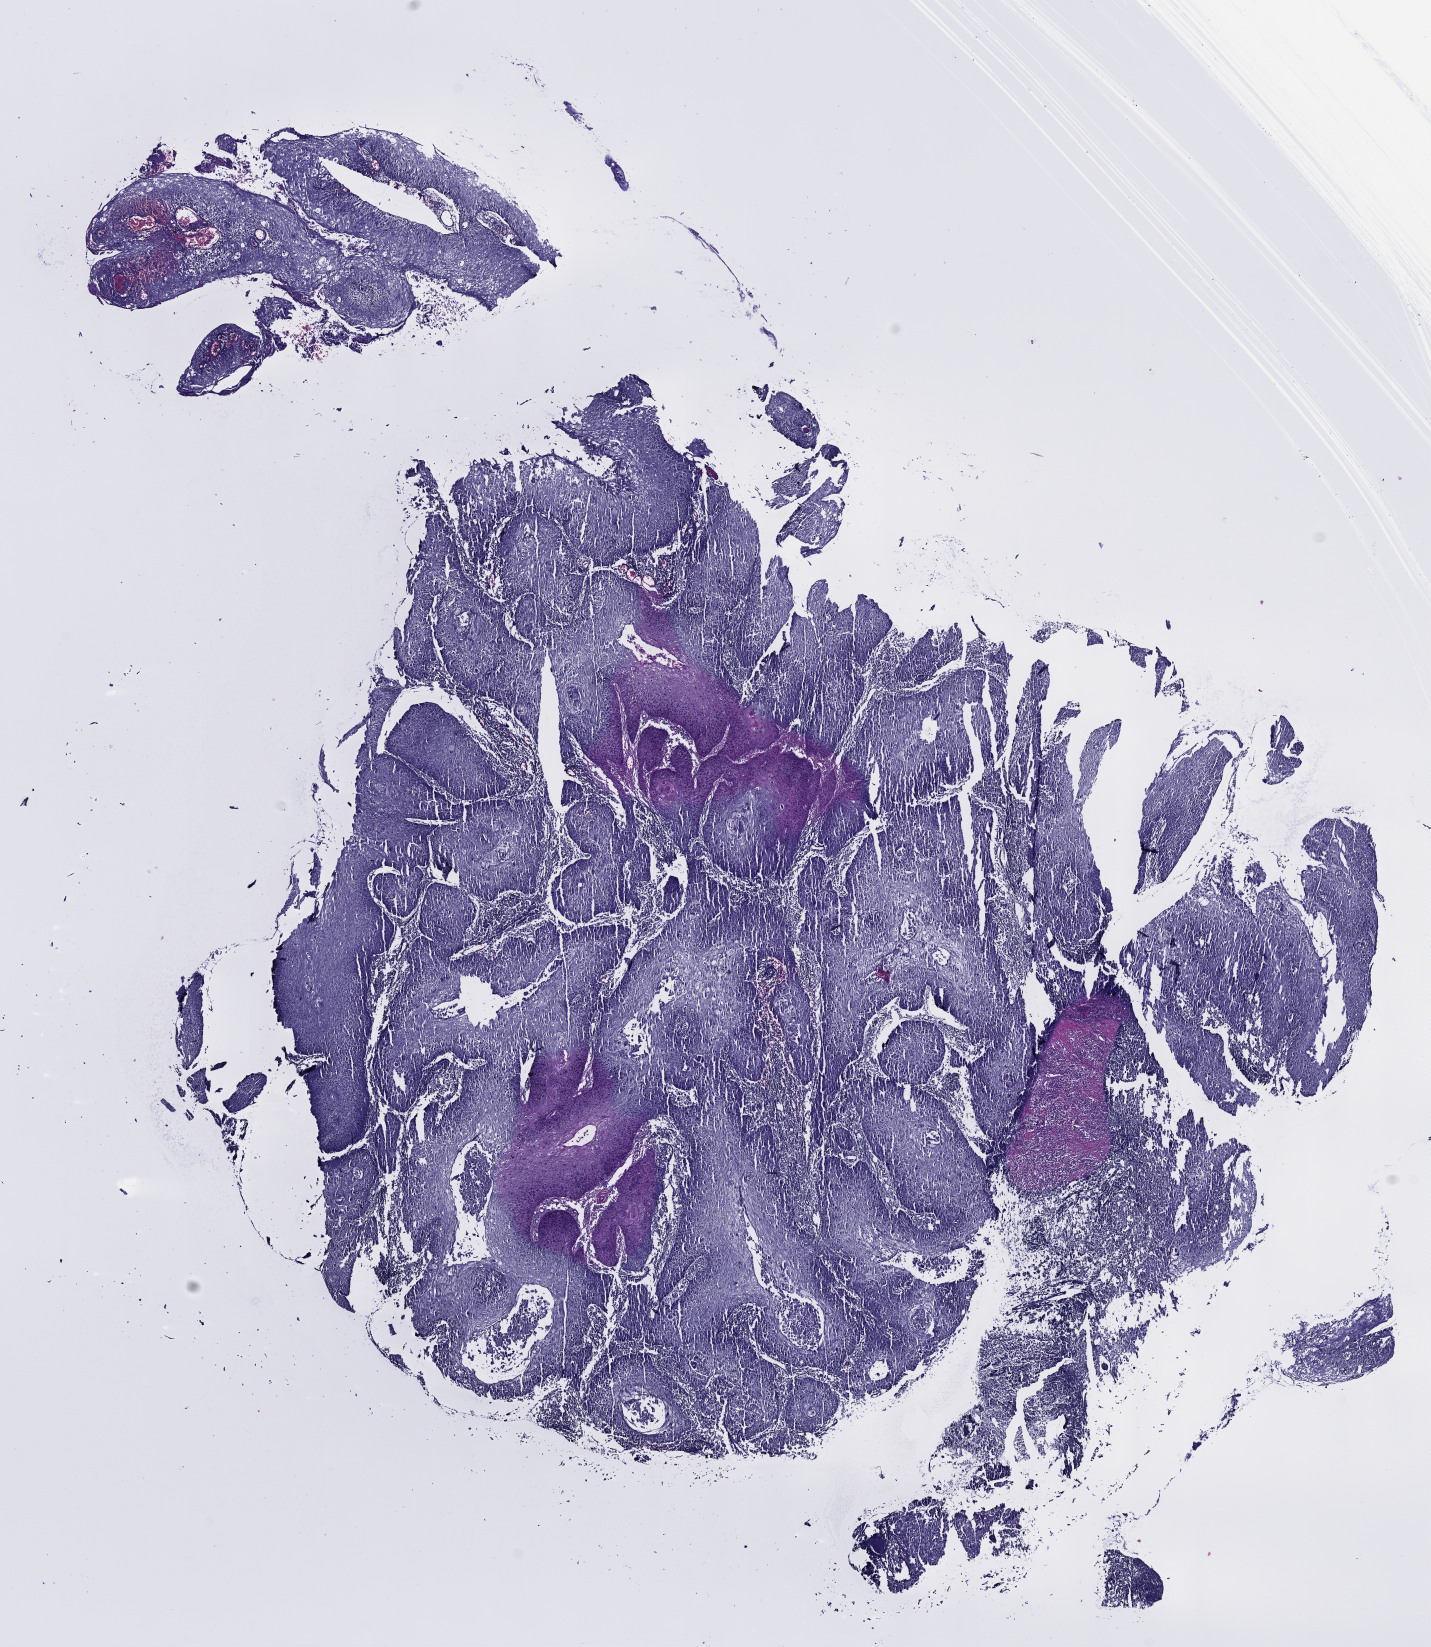
Hematoxylin and eosin (H&E) stained whole-slide image, whole scanned area (about 11.6 x 13.3 mm, acquisition: 40x scan) shown as a low-resolution overview; FFPE section; sample: primary tumour, head and neck. Female patient; age at initial diagnosis 80 years. Histologic grade: G1 (well differentiated).
Histologic diagnosis: Squamous cell carcinoma, NOS (floor of mouth, NOS). AJCC pathologic stage: III (7th edition).